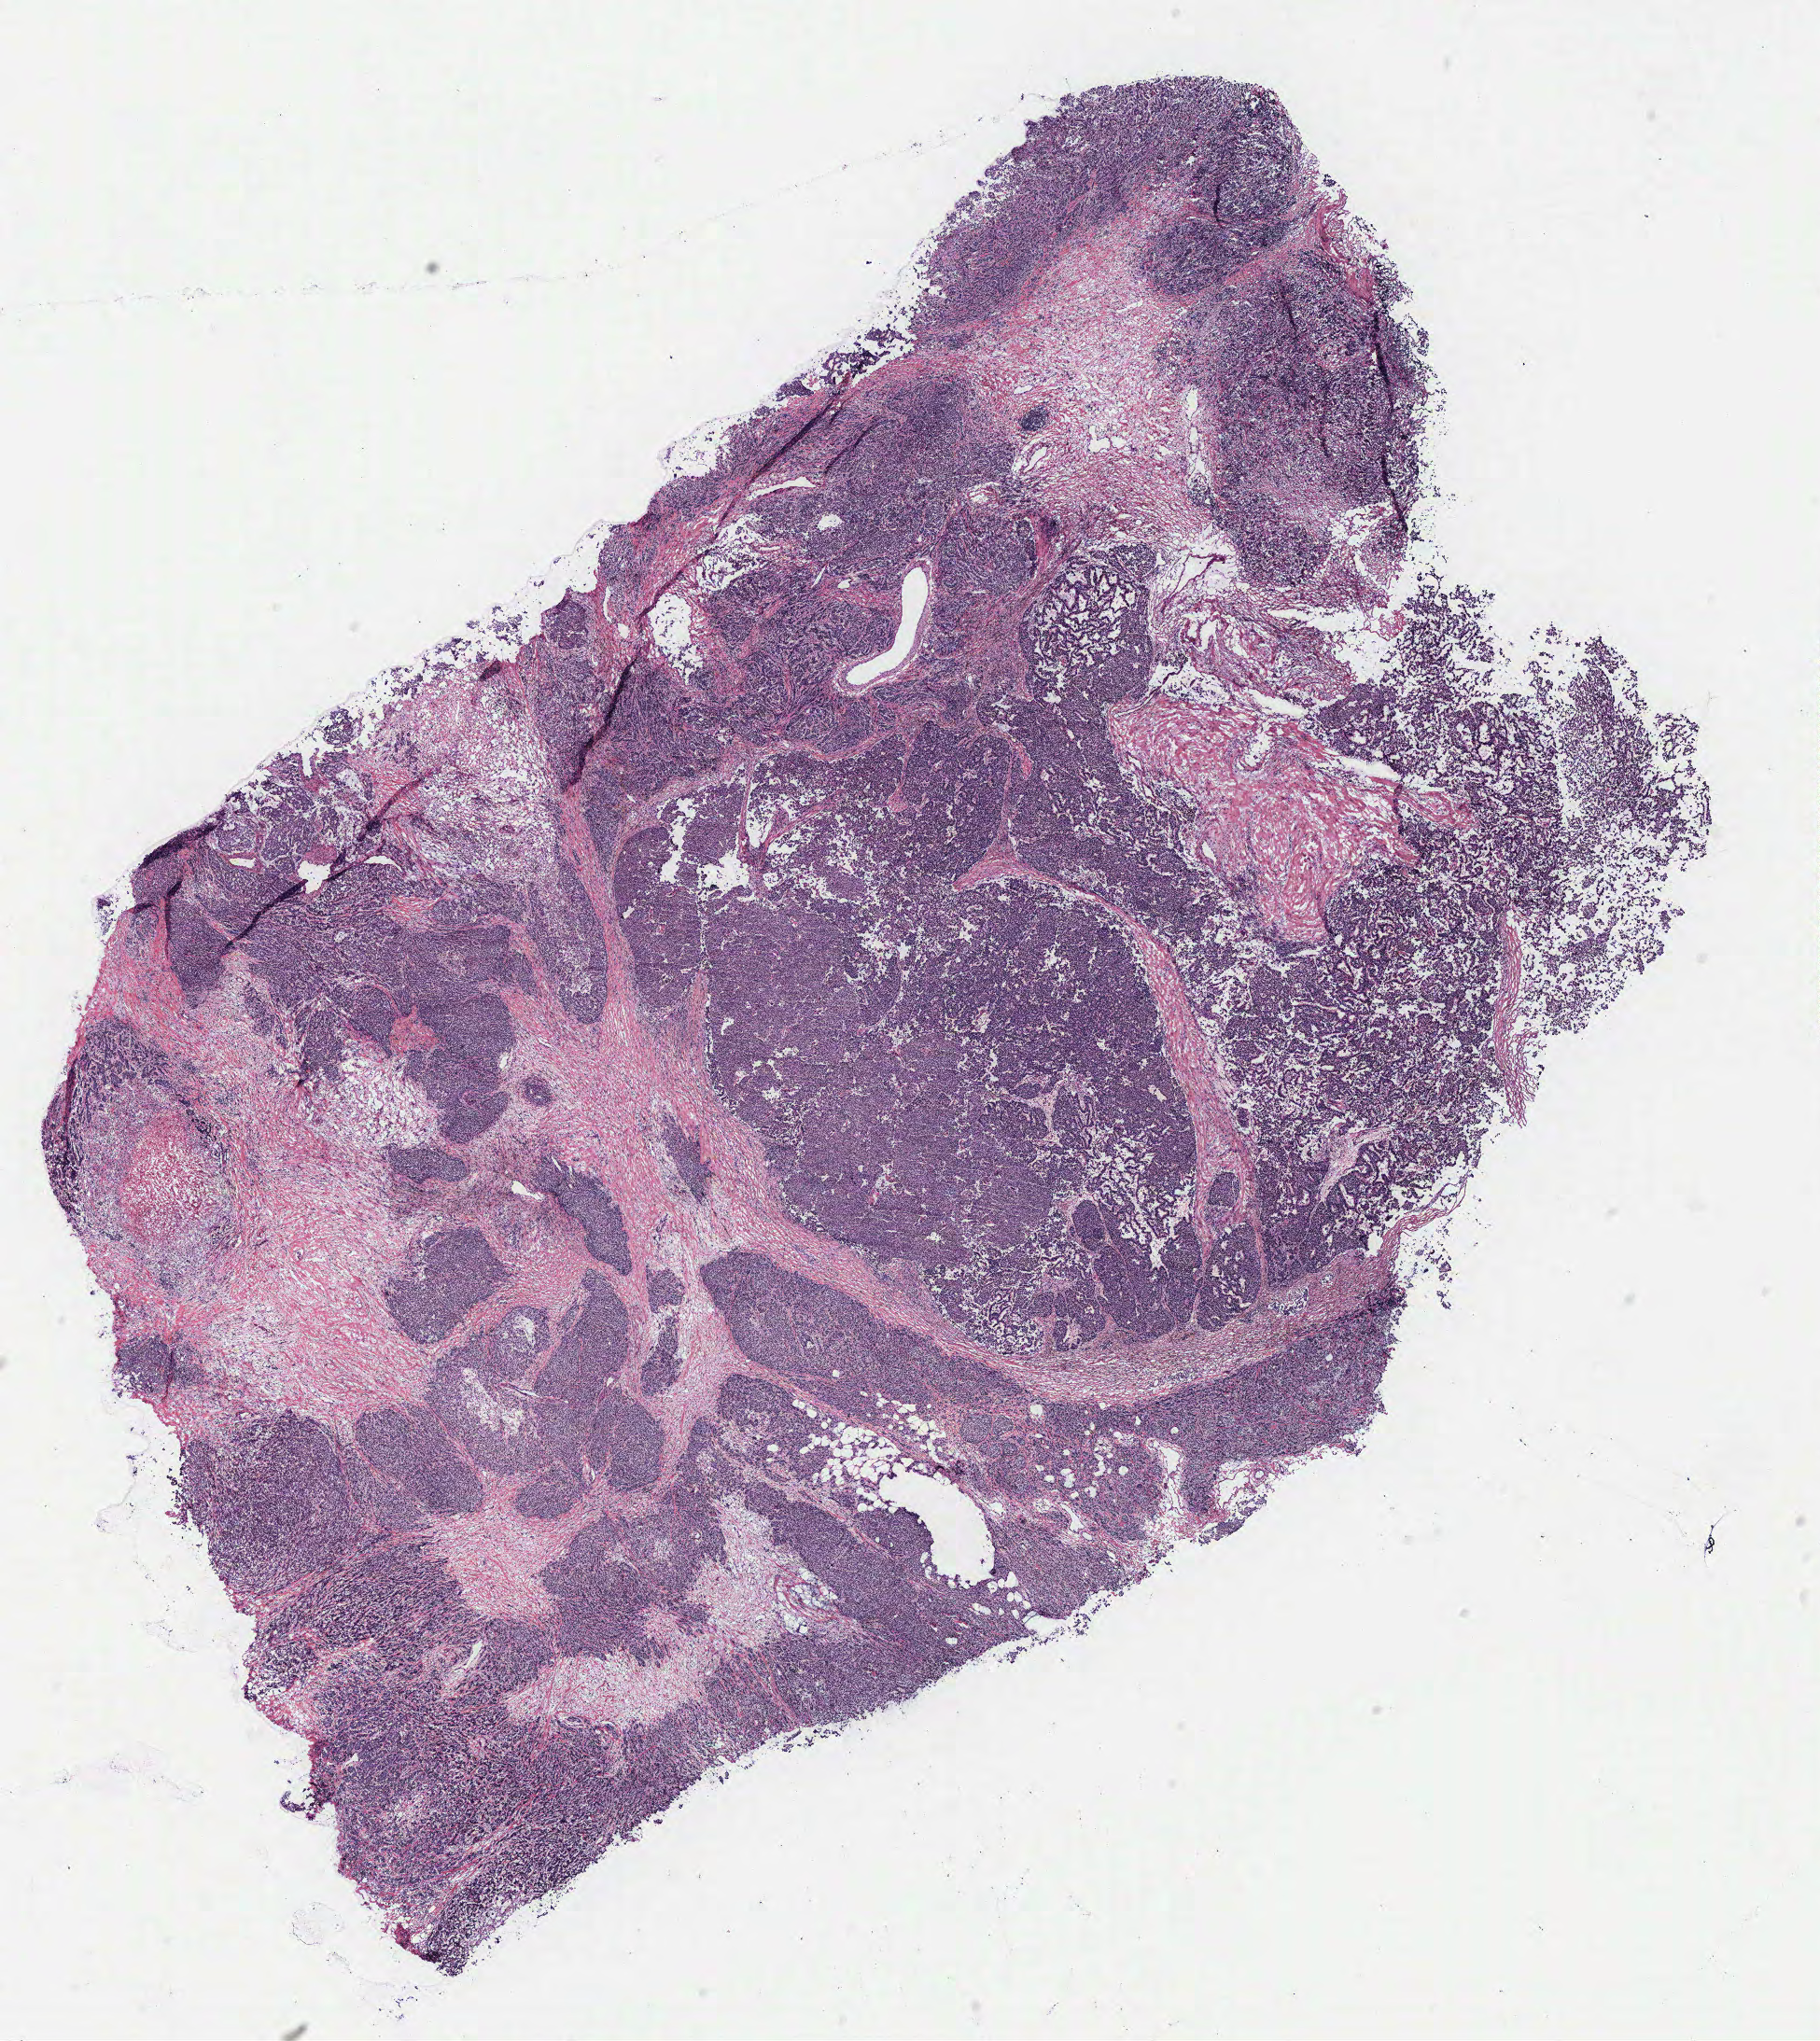
H&E-stained whole-slide image, low-resolution overview of the scanned area, about 15.6 x 17.5 mm (acquisition: 40x scan). Breast, tissue type not recorded. Patient: female, age 76 years.
Patient diagnosis: Infiltrating duct carcinoma, NOS.